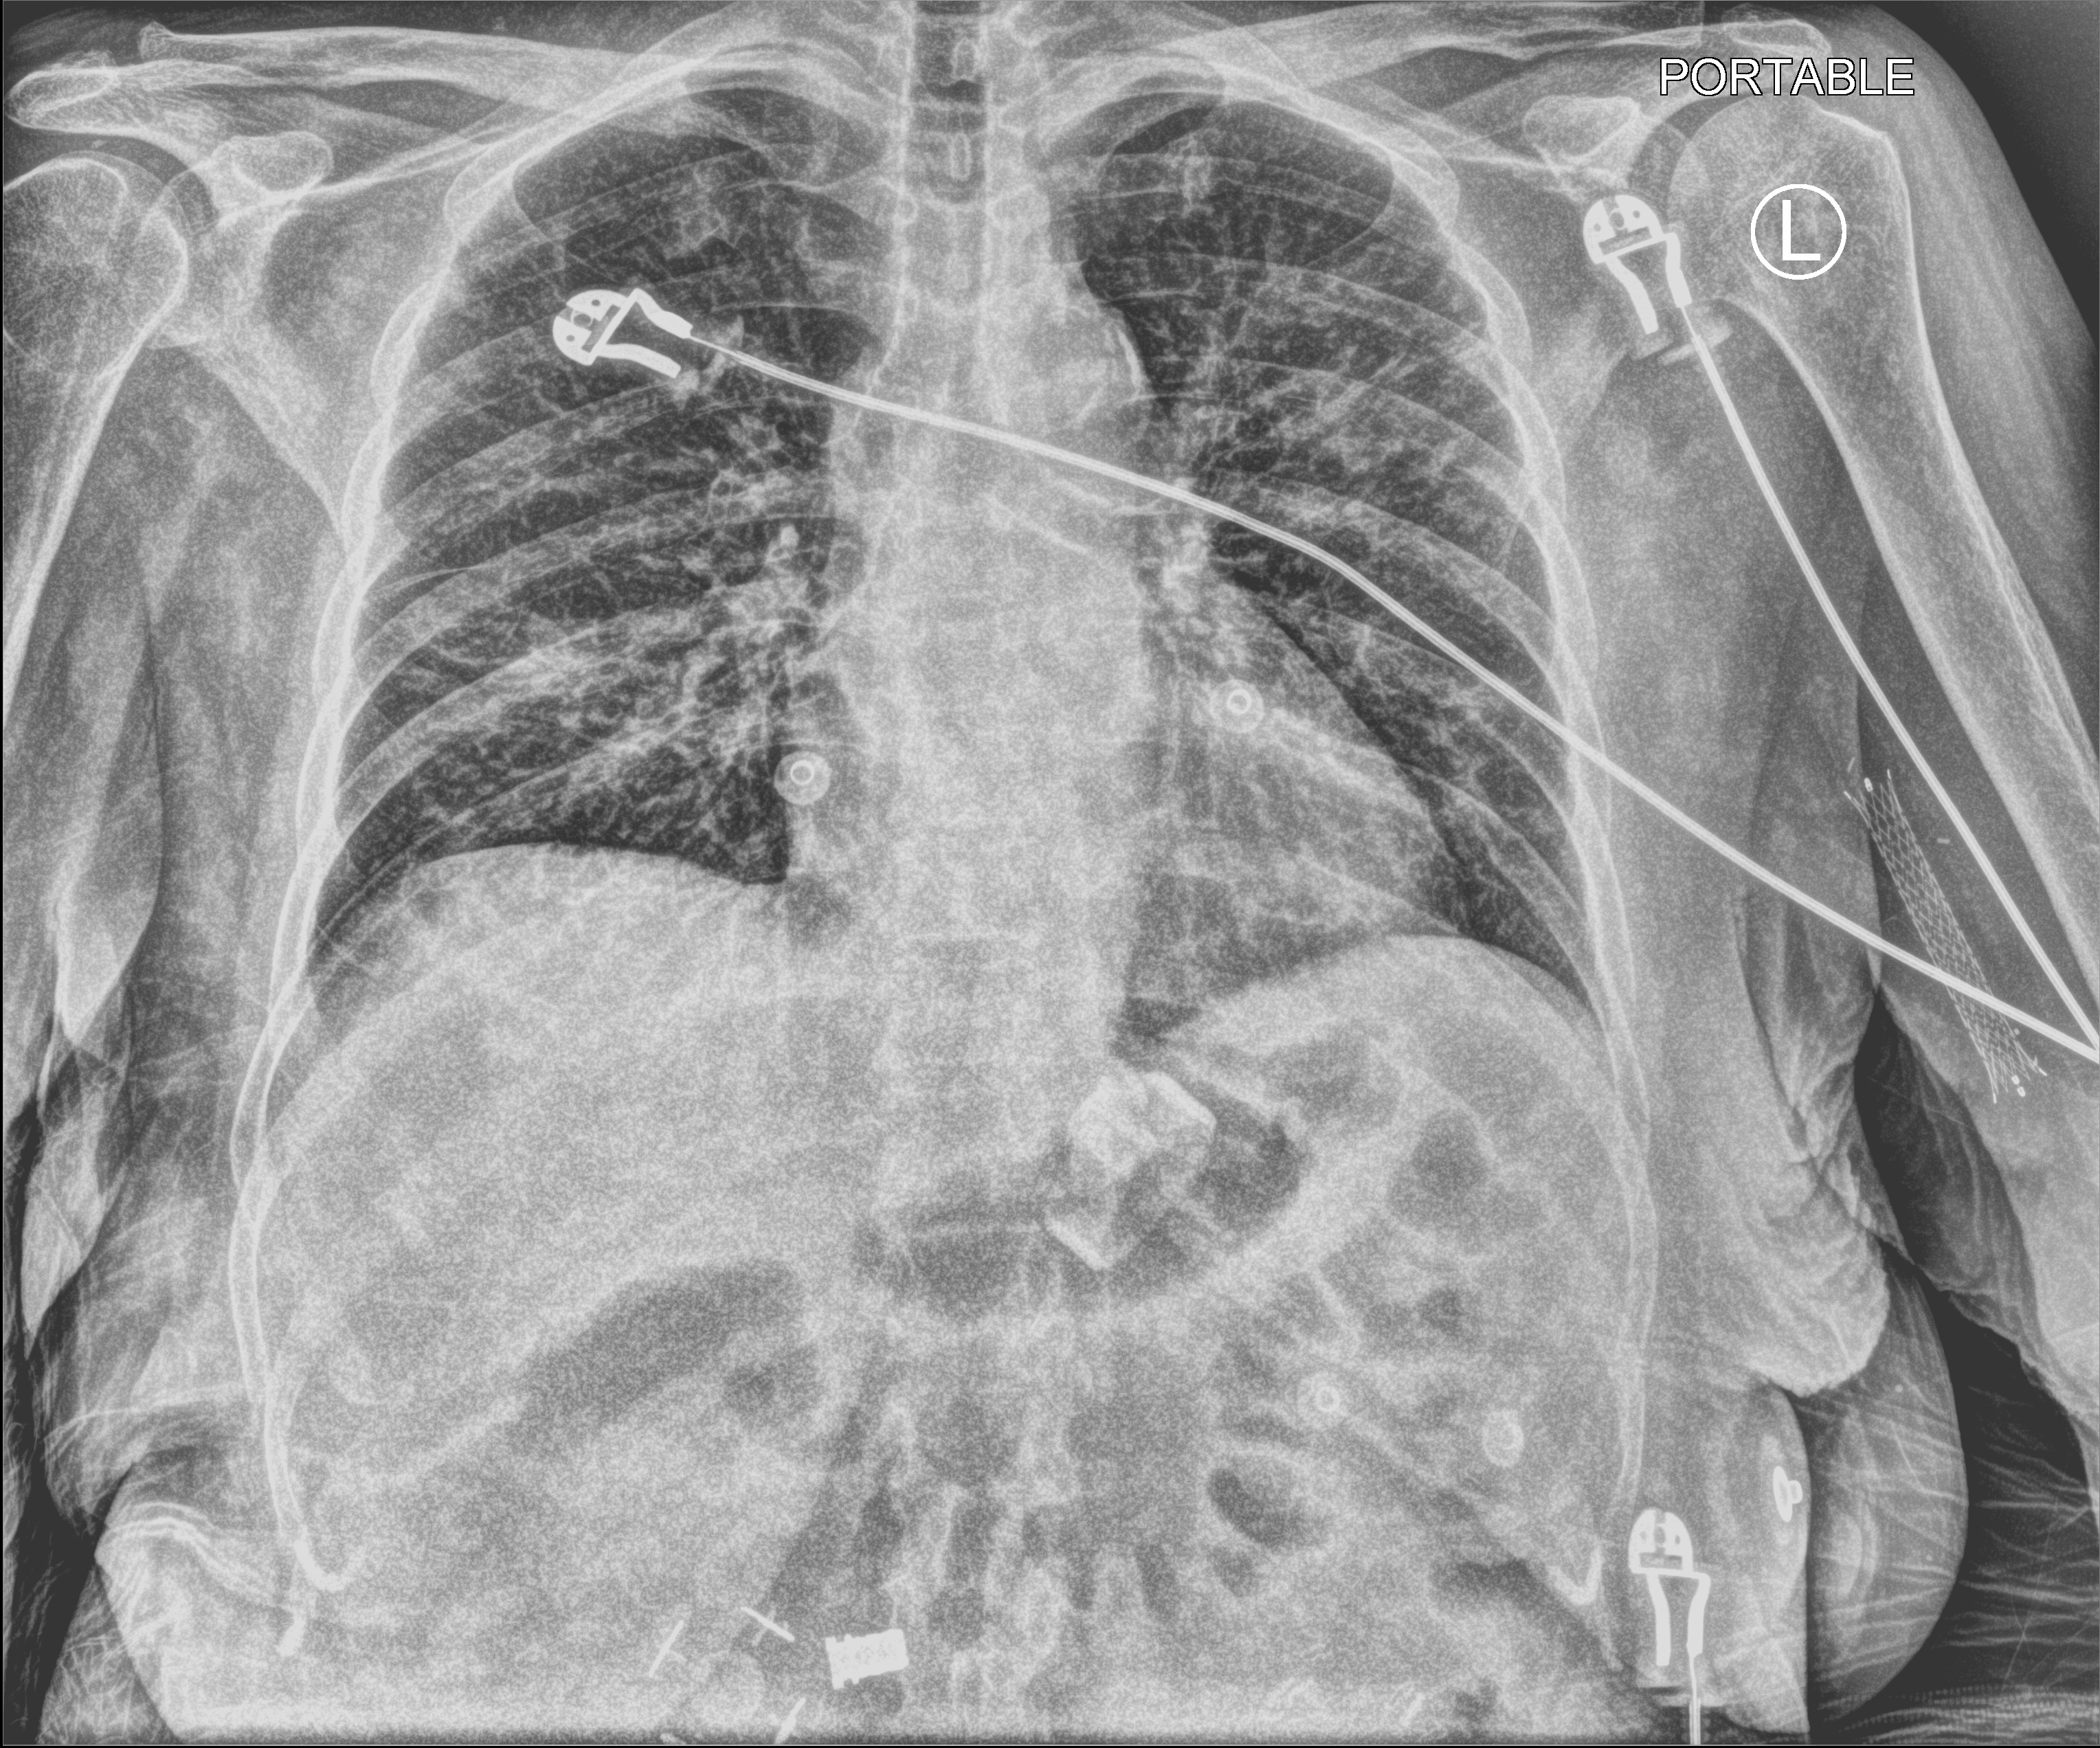
Portable chest radiograph, anteroposterior (AP) projection. Patient hospitalised with COVID-19; female, aged 60–74 years.
From the hospital-stay record, not from the radiograph (when in the stay this image was taken is not recorded): admitted to intensive care during this hospital stay: no; length of hospital stay: 6 days.